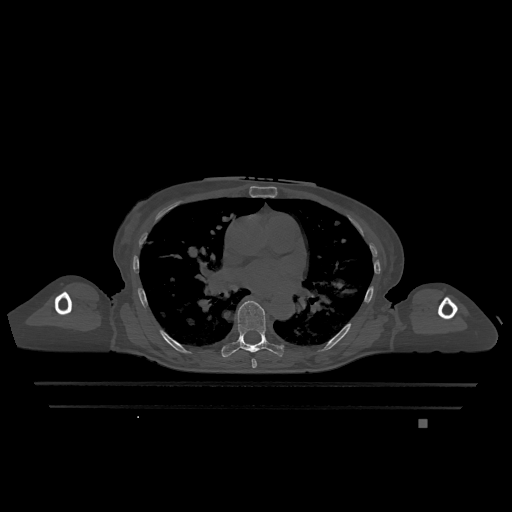
CT including the spine, one axial slice. Position 744 of 1317 along the scan axis. Bone window (W 1800 / L 400 HU). 512 × 512 image matrix, field of view 500 × 500 mm. Female patient, age 74 years. From the clinical record (not read from this slice): primary cancer: lung; vertebrae with lytic lesions (as recorded): T1, T4, T5, T6, L4, L5.
Annotated regions visible in this slice (semi-automatically segmented with operator editing):
- T6 vertebra: bounding box (x1, y1, x2, y2) in pixels: (252, 358, 257, 368)
- T7 vertebra: (221, 301, 284, 358)